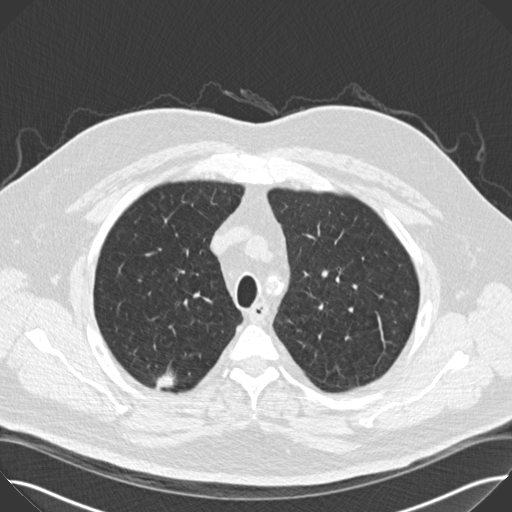
Low-dose screening chest CT, axial slice; first (baseline) screen; lung window (W 1500 / L -600 HU); 2 mm slice thickness; 120 kVp; slice 125 of 158 in the series; 512 × 512 image matrix, field of view 380 × 380 mm. Male, age 65 years at enrolment.
• Expert reader's lesion annotation, bounding box (x1, y1, x2, y2) in pixels: (148, 359, 191, 415).
• The screening reader recorded 2 non-calcified nodules or masses ≥4 mm on this exam; which of them this box marks is not recorded.
• Official screen result: positive, change unspecified: nodule(s) >= 4 mm or enlarging nodule(s), mass(es), or other non-specific abnormalities suspicious for lung cancer.
• Later outcome: lung cancer diagnosed 47 days after this screen — bronchiolo-alveolar adenocarcinoma, NOS, right upper lobe, moderately differentiated (G2), stage IIA (AJCC 6th edition), 14 mm at pathology.